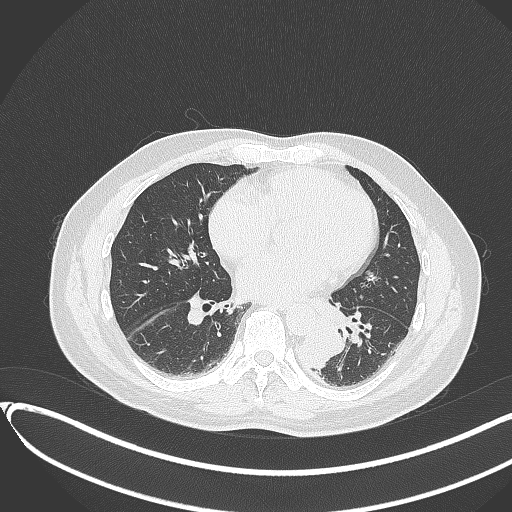
Chest CT, one axial slice; position 141 of 417 along the scan axis; 120 kVp; lung window (W 1500 / L -600 HU); 1 mm slice thickness; 512 × 512 image matrix, field of view 400 × 400 mm. Patient: male, 54 years. From the clinical record (not read from this slice): clinical TNM (as recorded): T3 N0 M0.
Annotated regions visible in this slice (bounding box drawn by a radiologist):
- lung tumour (recorded histology: squamous cell carcinoma): bounding box (x1, y1, x2, y2) in pixels: (299, 321, 344, 368)